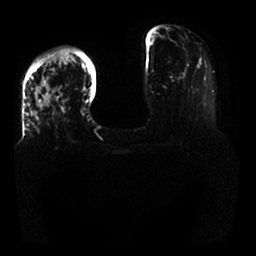
Breast MRI, one axial slice; position 7 of 25 along the scan axis; diffusion-weighted series; image 2 of 4 stored at this slice position (different b-values; order by instance number); 1.5 T; 256 × 256 image matrix, field of view 350 × 350 mm. Female patient.
Annotated regions visible in this slice (expert manual segmentation):
- tumour on diffusion-weighted imaging: bounding box (x1, y1, x2, y2) in pixels: (32, 52, 73, 122)